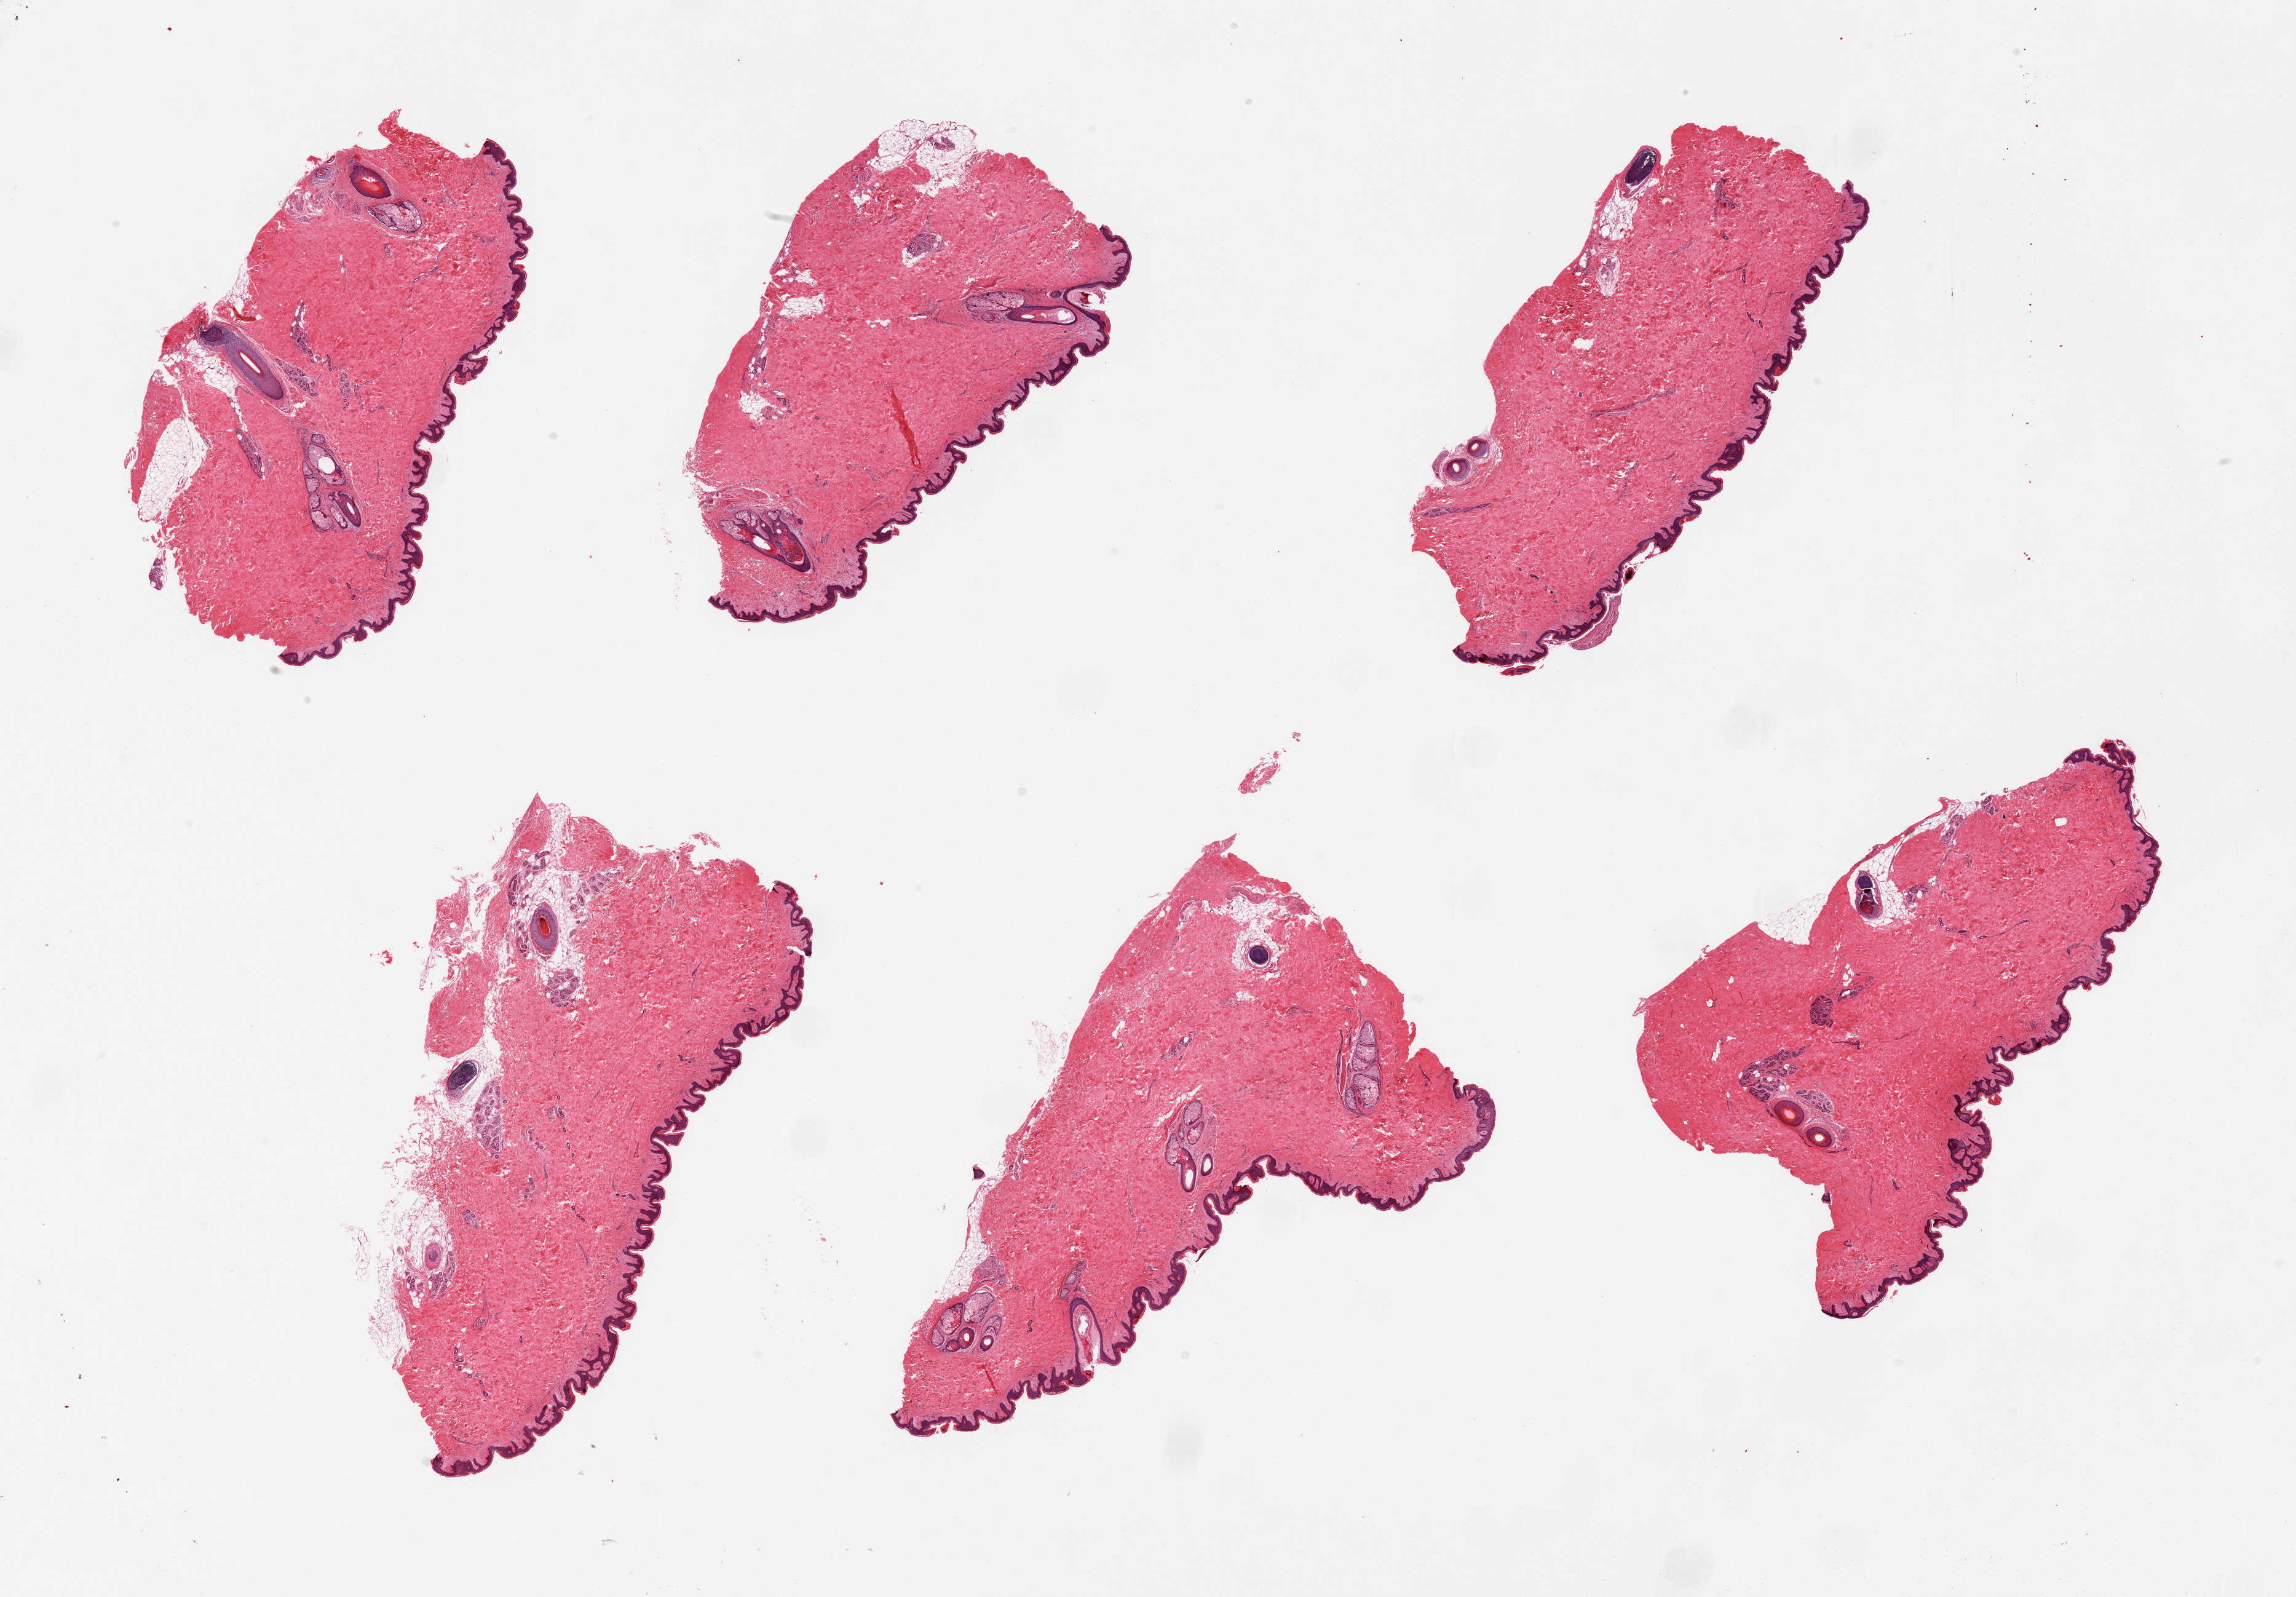
Hematoxylin and eosin (H&E) whole-slide image — low-resolution overview of the scanned area, about 29.5 x 20.5 mm (slide scanned at 20x). PAXgene-fixed, paraffin-embedded tissue. Section of skin of suprapubic region (target tissue). Tissue donor sample. Donor sex: male.
Pathologist's review note for this sample: 6 pieces, few with minimal attached fat.